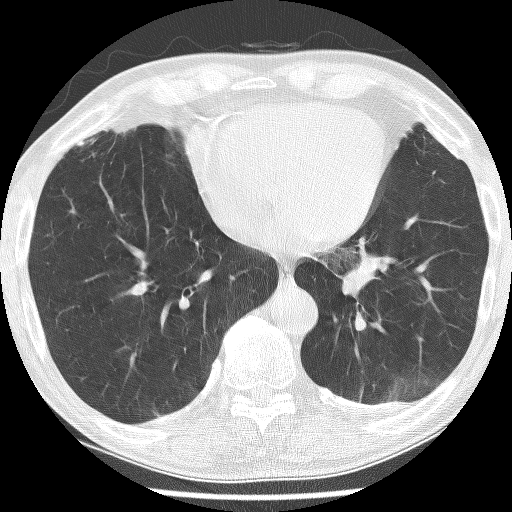
Axial slice from a low-dose chest CT screening exam, first (baseline) screen, lung window (W 1500 / L -600 HU), 2.5 mm slice thickness, lung (sharp) reconstruction kernel (BONE), 120 kVp, slice 166 of 226 in the series. Male, age 74 years at enrolment. Current smoker at enrolment.
- Expert reader's lesion annotation, bounding box [x1, y1, x2, y2] px = [319, 231, 427, 325].
- The exam's reader record, not a measurement of the box and not confirmed to be the same lesion: non-calcified nodule or mass ≥4 mm, left lower lobe, 30 × 27 mm, spiculated (stellate) margins, soft tissue attenuation.
- Official screen result: positive, change unspecified: nodule(s) >= 4 mm or enlarging nodule(s), mass(es), or other non-specific abnormalities suspicious for lung cancer.
- Lung cancer was diagnosed 151 days after this screen: adenocarcinoma, NOS, left lower lobe, stage IIIA (AJCC 6th edition), 49 mm at pathology.